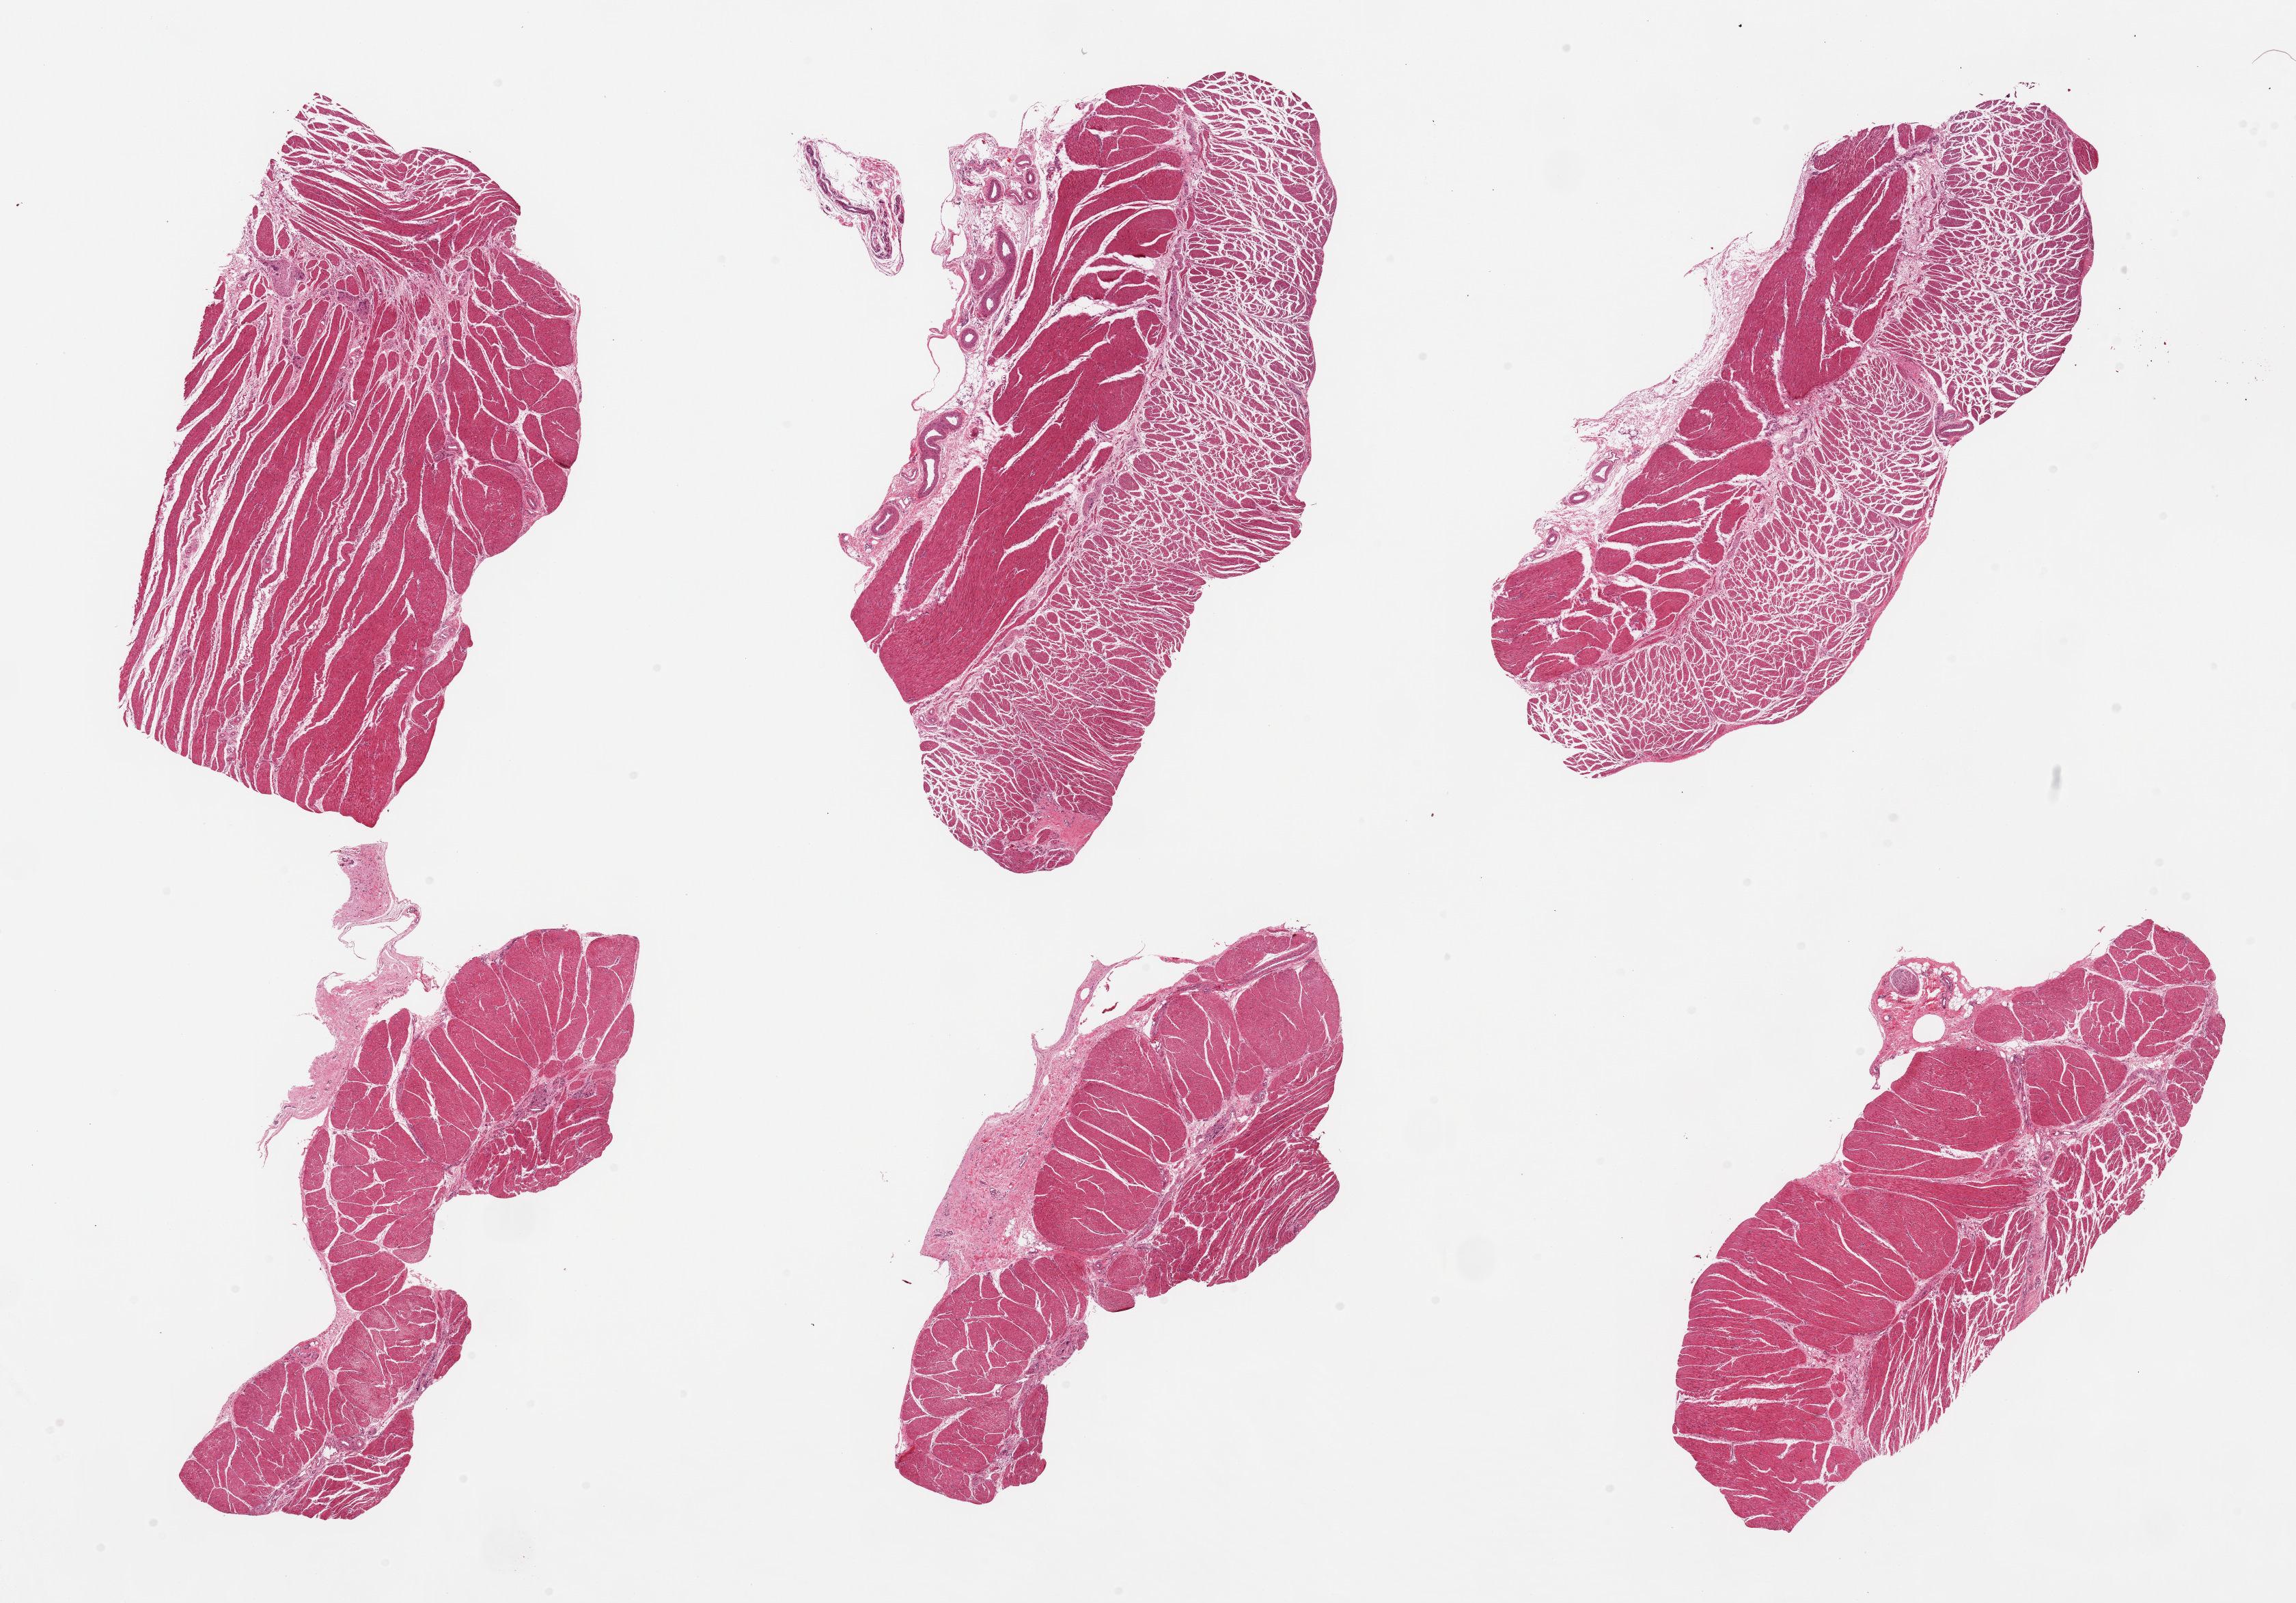
Digitized haematoxylin and eosin-stained section, brightfield — shown as a low-resolution overview of the whole scanned area (about 26.6 x 18.6 mm); PAXgene-fixed, paraffin-embedded tissue; target tissue: esophageal muscle; tissue donor sample. Male donor.
- reviewer comment on this tissue sample: 6 pieces; target muscularis present